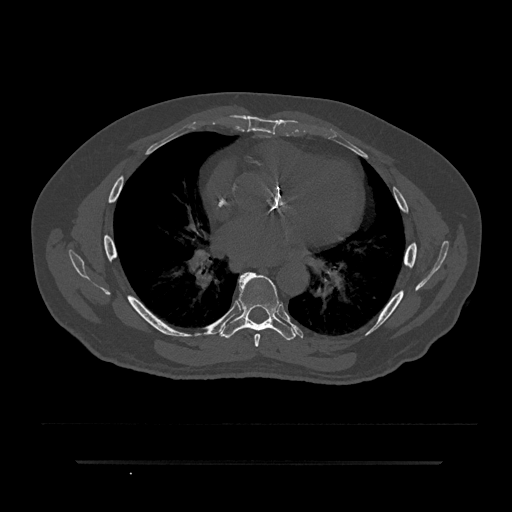
CT including the spine, one axial slice. Slice 492 of 797 in the series (ordered by position). Reconstruction kernel Br40s/3. 120 kVp. Bone window (W 1800 / L 400 HU). 0.5 mm slice thickness. 512 × 512 image matrix, field of view 464 × 464 mm. Patient: male, 59 years. From the clinical record (not read from this slice): primary cancer: bile ducts; vertebrae with lytic lesions (as recorded): T10.
Structures marked on this image (semi-automatically segmented with operator editing):
- T6 vertebra: bounding box [x1, y1, x2, y2] px = [240, 278, 261, 347]
- T7 vertebra: [220, 272, 296, 340]